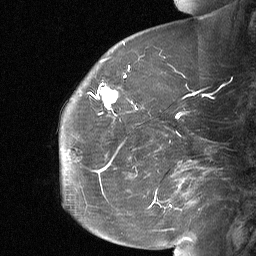
Breast MRI (dynamic contrast-enhanced), one sagittal slice; position 21 of 64 along the scan axis; dynamic contrast-enhanced study with each time point stored as its own series, time point 2 of 3 at this slice position (early post-contrast, ordered by acquisition time); 1.5 T; TE 4.8 ms, TR 27 ms; 2 mm slice thickness; 256 × 256 image matrix. Patient: female, 60 years. Case-level facts recorded for this patient, not image findings: setting: breast cancer imaged before/during neoadjuvant chemotherapy; receptor status: HR-positive, HER2-negative.
Structures marked on this image (semi-automatic segmentation, software-assisted and operator-edited):
- analysis volume of interest (the breast-tissue region the enhancement analysis was run in; not a lesion): bounding box [x1, y1, x2, y2] px = [92, 70, 134, 112]
- tumour enhancement mask (voxels above the 90 % enhancement threshold inside the analysis volume of interest): [94, 76, 125, 110]